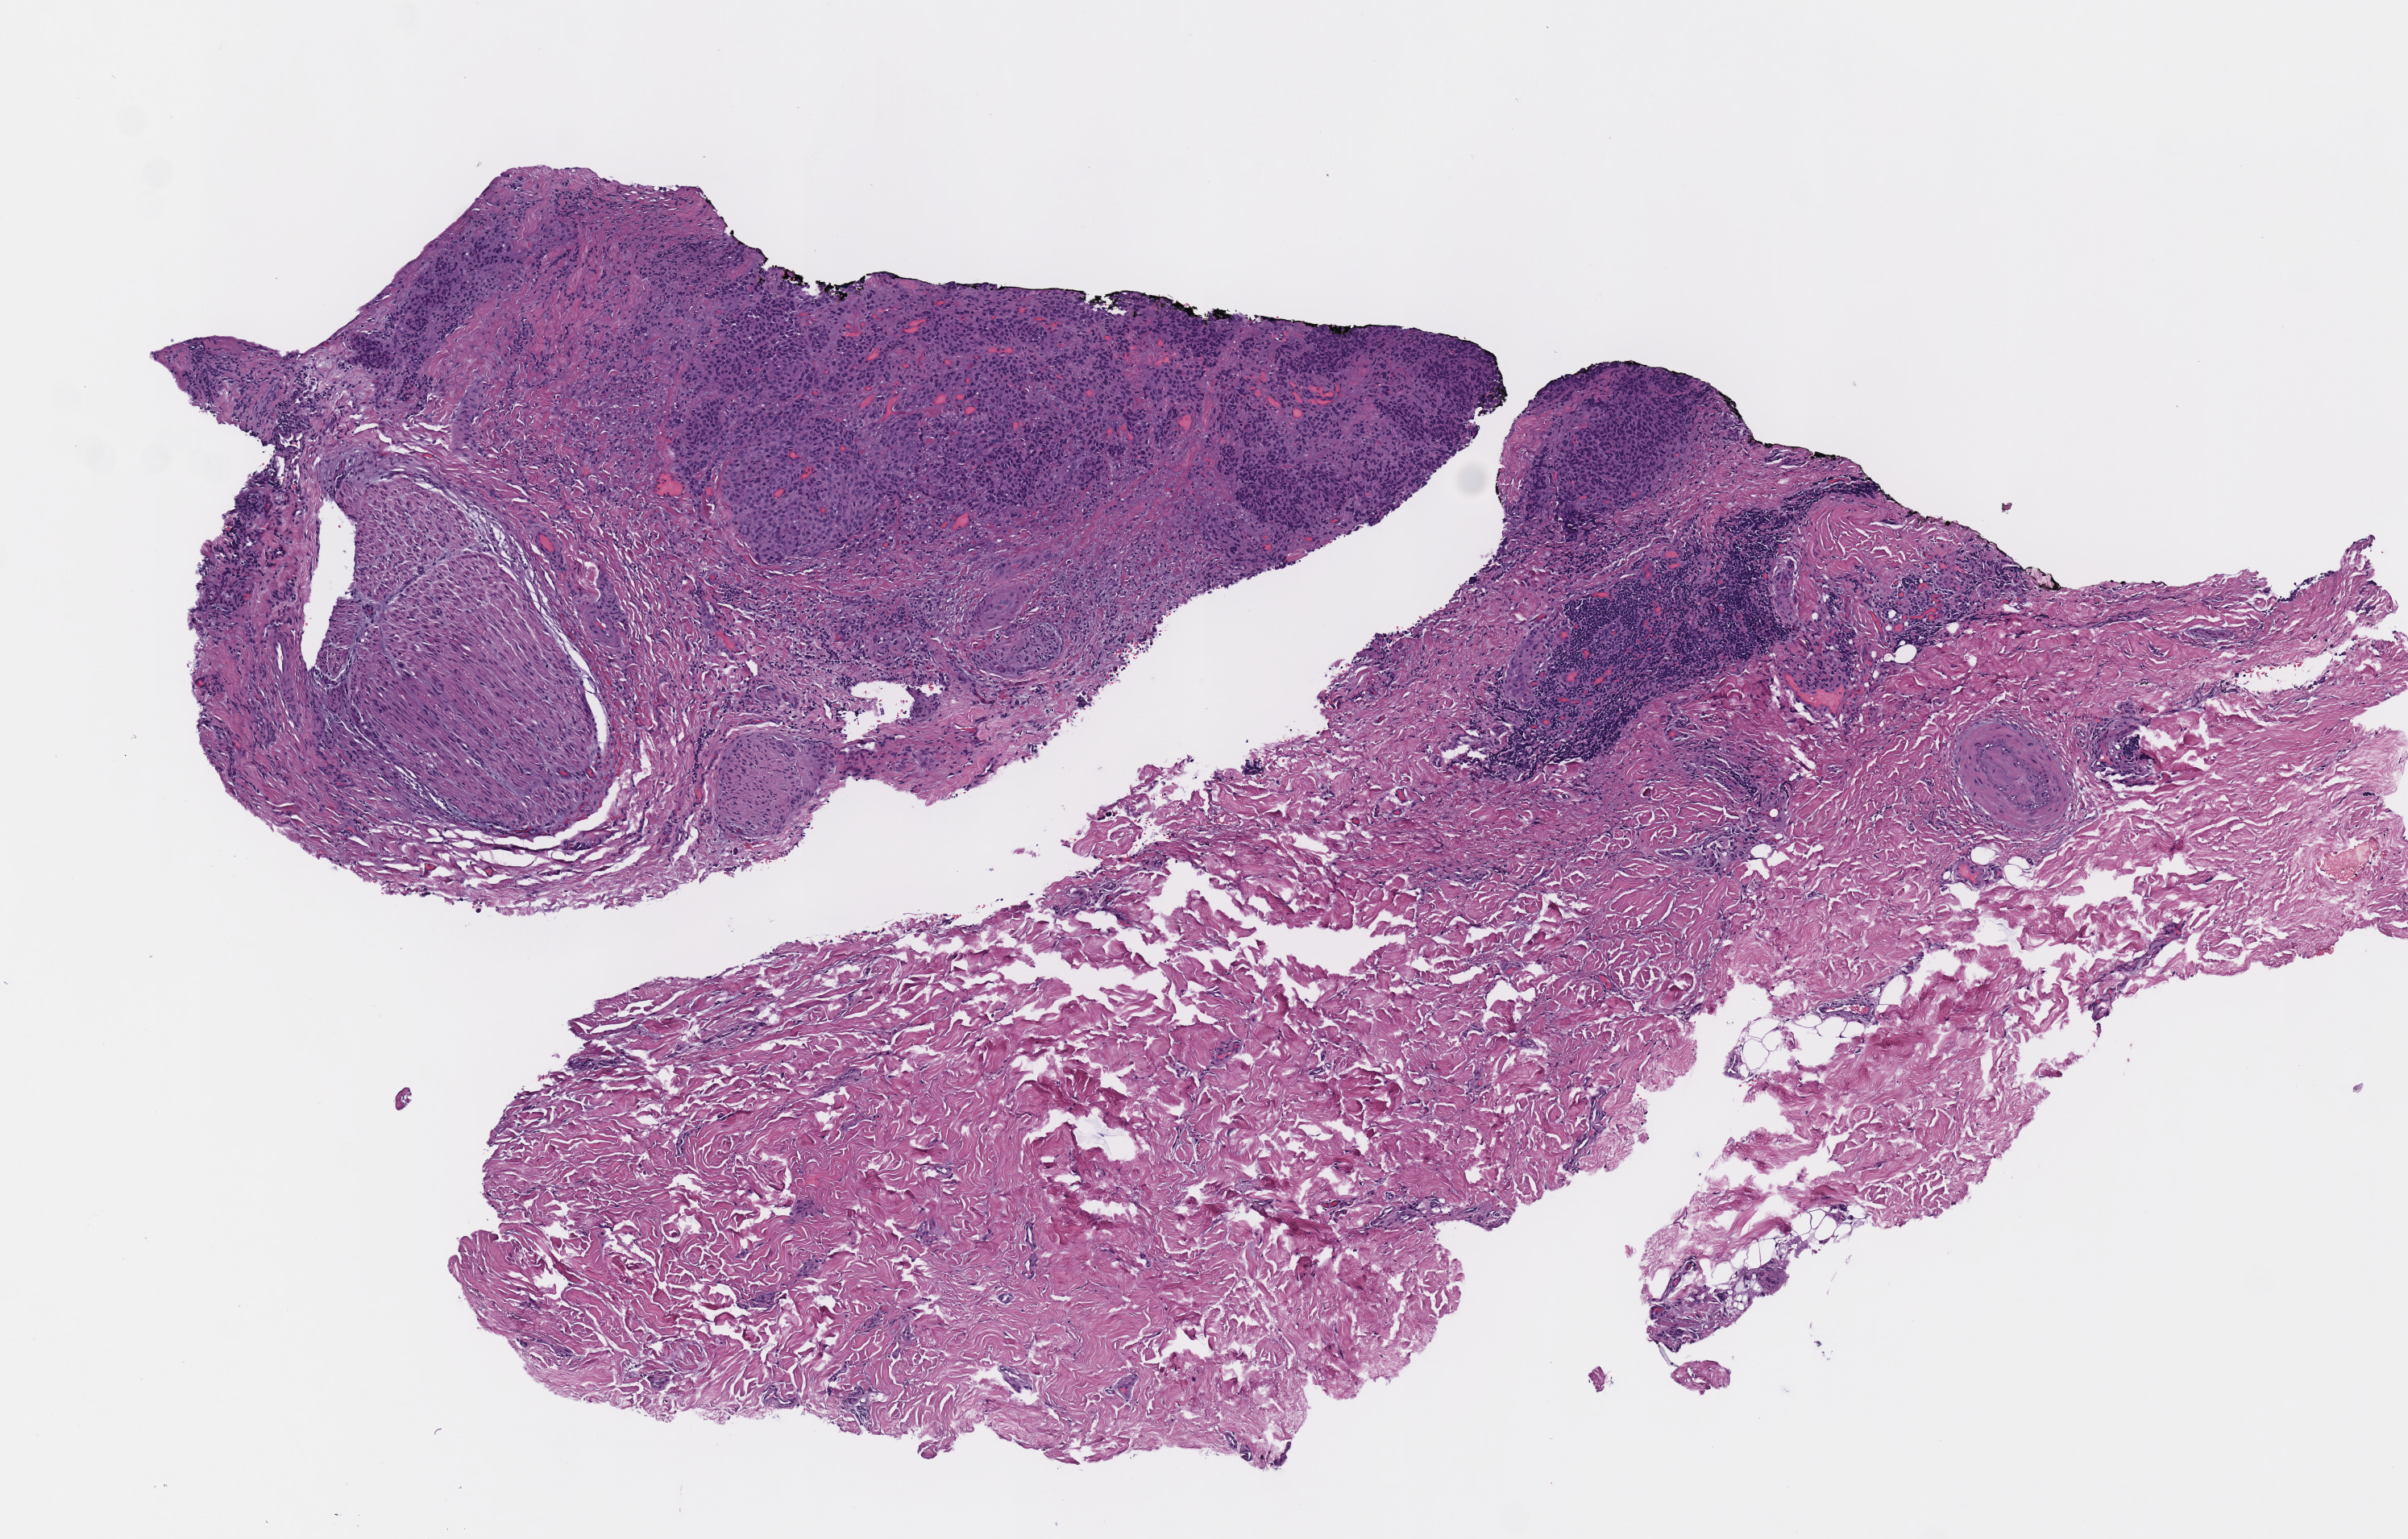
Digitized H&E tissue section (whole slide) — whole scanned area (about 5.9 x 3.8 mm, acquisition: 40x scan) shown as a low-resolution overview; FFPE section; primary tumour sample from the skin. Male patient; age at initial diagnosis 68 years.
Diagnosis: Malignant melanoma, NOS.